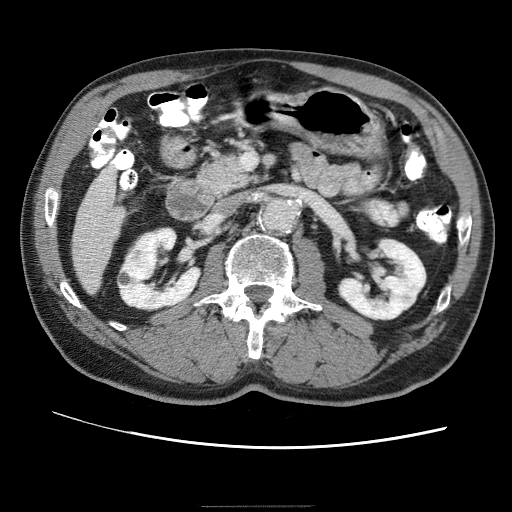
Contrast-enhanced abdominal CT (liver protocol), one axial slice; position 10 of 75 along the scan axis; reconstruction kernel STANDARD; 120 kVp; one of 2 acquisitions stored at this slice position; soft-tissue window (W 400 / L 40 HU); 2.5 mm slice thickness; 512 × 512 image matrix, field of view 360 × 360 mm. Case-level facts recorded for this patient, not image findings: diagnosis: hepatocellular carcinoma (patient treated with transarterial chemoembolisation; whether this scan precedes or follows treatment is not stated here); TNM stage (as recorded): Stage-II; Child-Pugh class: A; tumour nodularity: multinodular; tumour size: 2 cm.
Outlined on this slice (semi-automatic segmentation, software-assisted and operator-edited):
- liver parenchyma outside the tumour (the mass and vessels are separate outlines, so this box may not span the whole liver): box from (x=72, y=170) to (x=117, y=282) px
- liver vessels: (x=88, y=173)–(x=114, y=229)